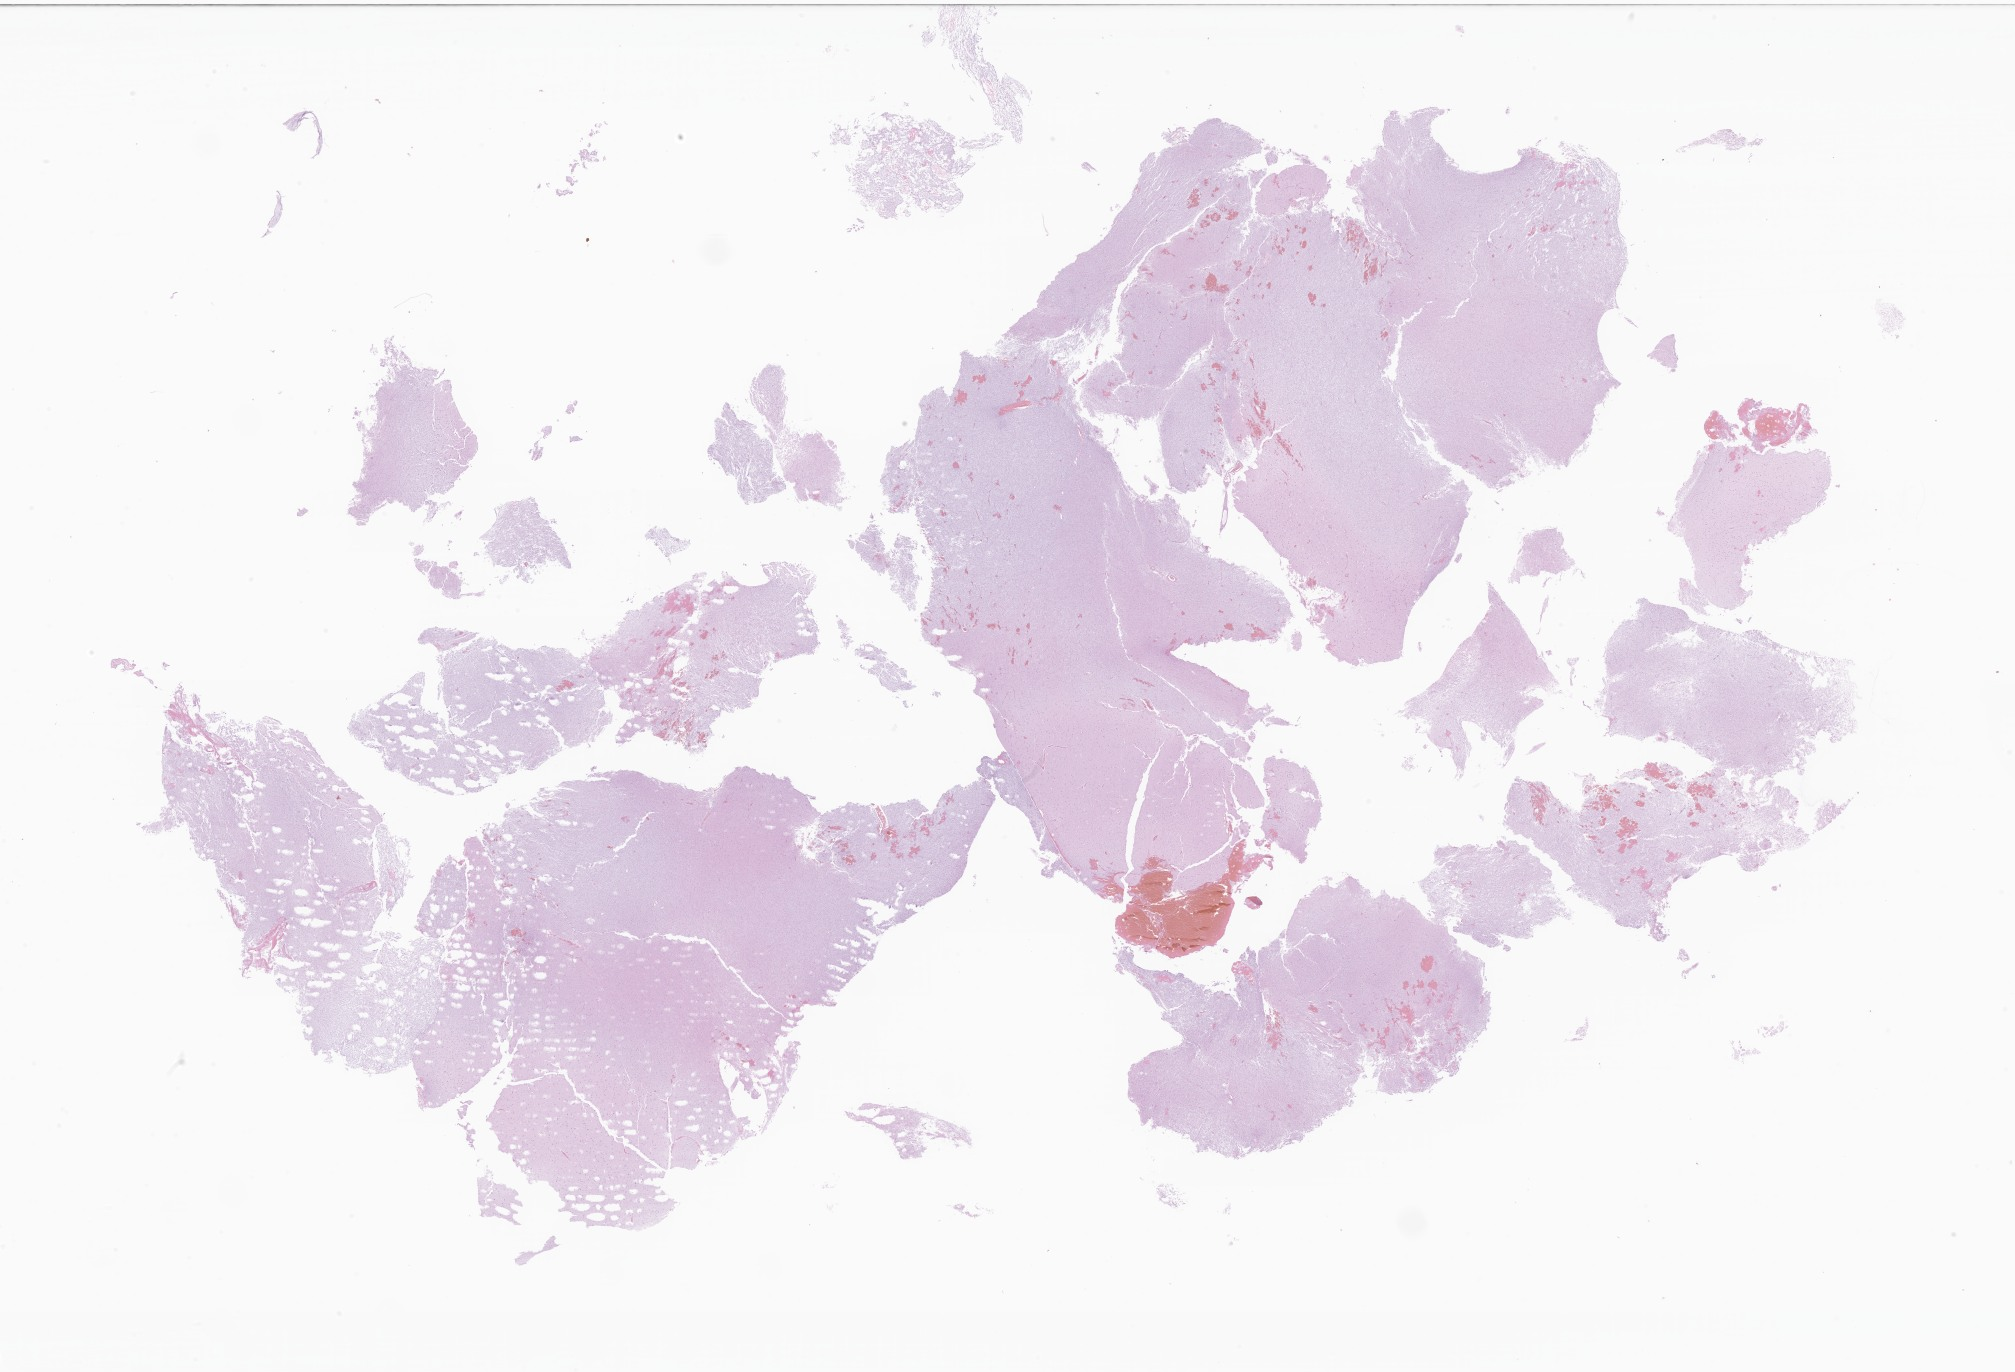
Whole-slide image, H&E stain of tumor tissue from the brain, shown as a low-resolution overview of the whole scanned area (about 34.0 x 23.1 mm); formalin-fixed, paraffin-embedded (FFPE) tissue. Patient male; age 897 days (about 2.5 years).
- recorded diagnosis: Ganglioglioma, NOS